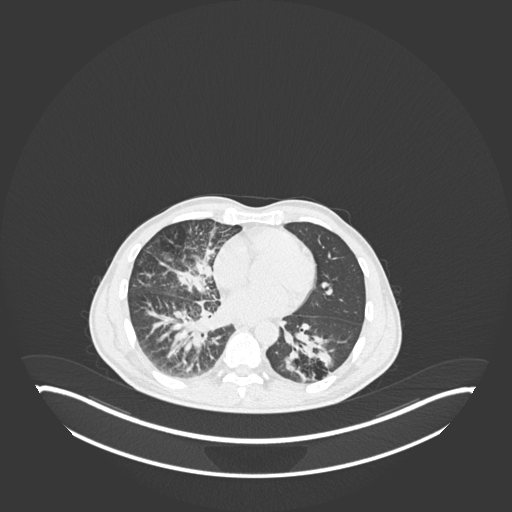
Chest CT, one axial slice. Slice 100 of 237 in the series (ordered by position). Reconstruction kernel B30f. Lung window (W 1500 / L -600 HU). 1 mm slice thickness. 512 × 512 image matrix. Male patient, age 49 years. Case-level facts recorded for this patient, not image findings: clinical TNM (as recorded): T2b N1 M0.
Outlined on this slice (rectangle marked by the reading radiologist):
- lung tumour (recorded histology: adenocarcinoma): bounding box [x1, y1, x2, y2] px = [284, 328, 338, 386]